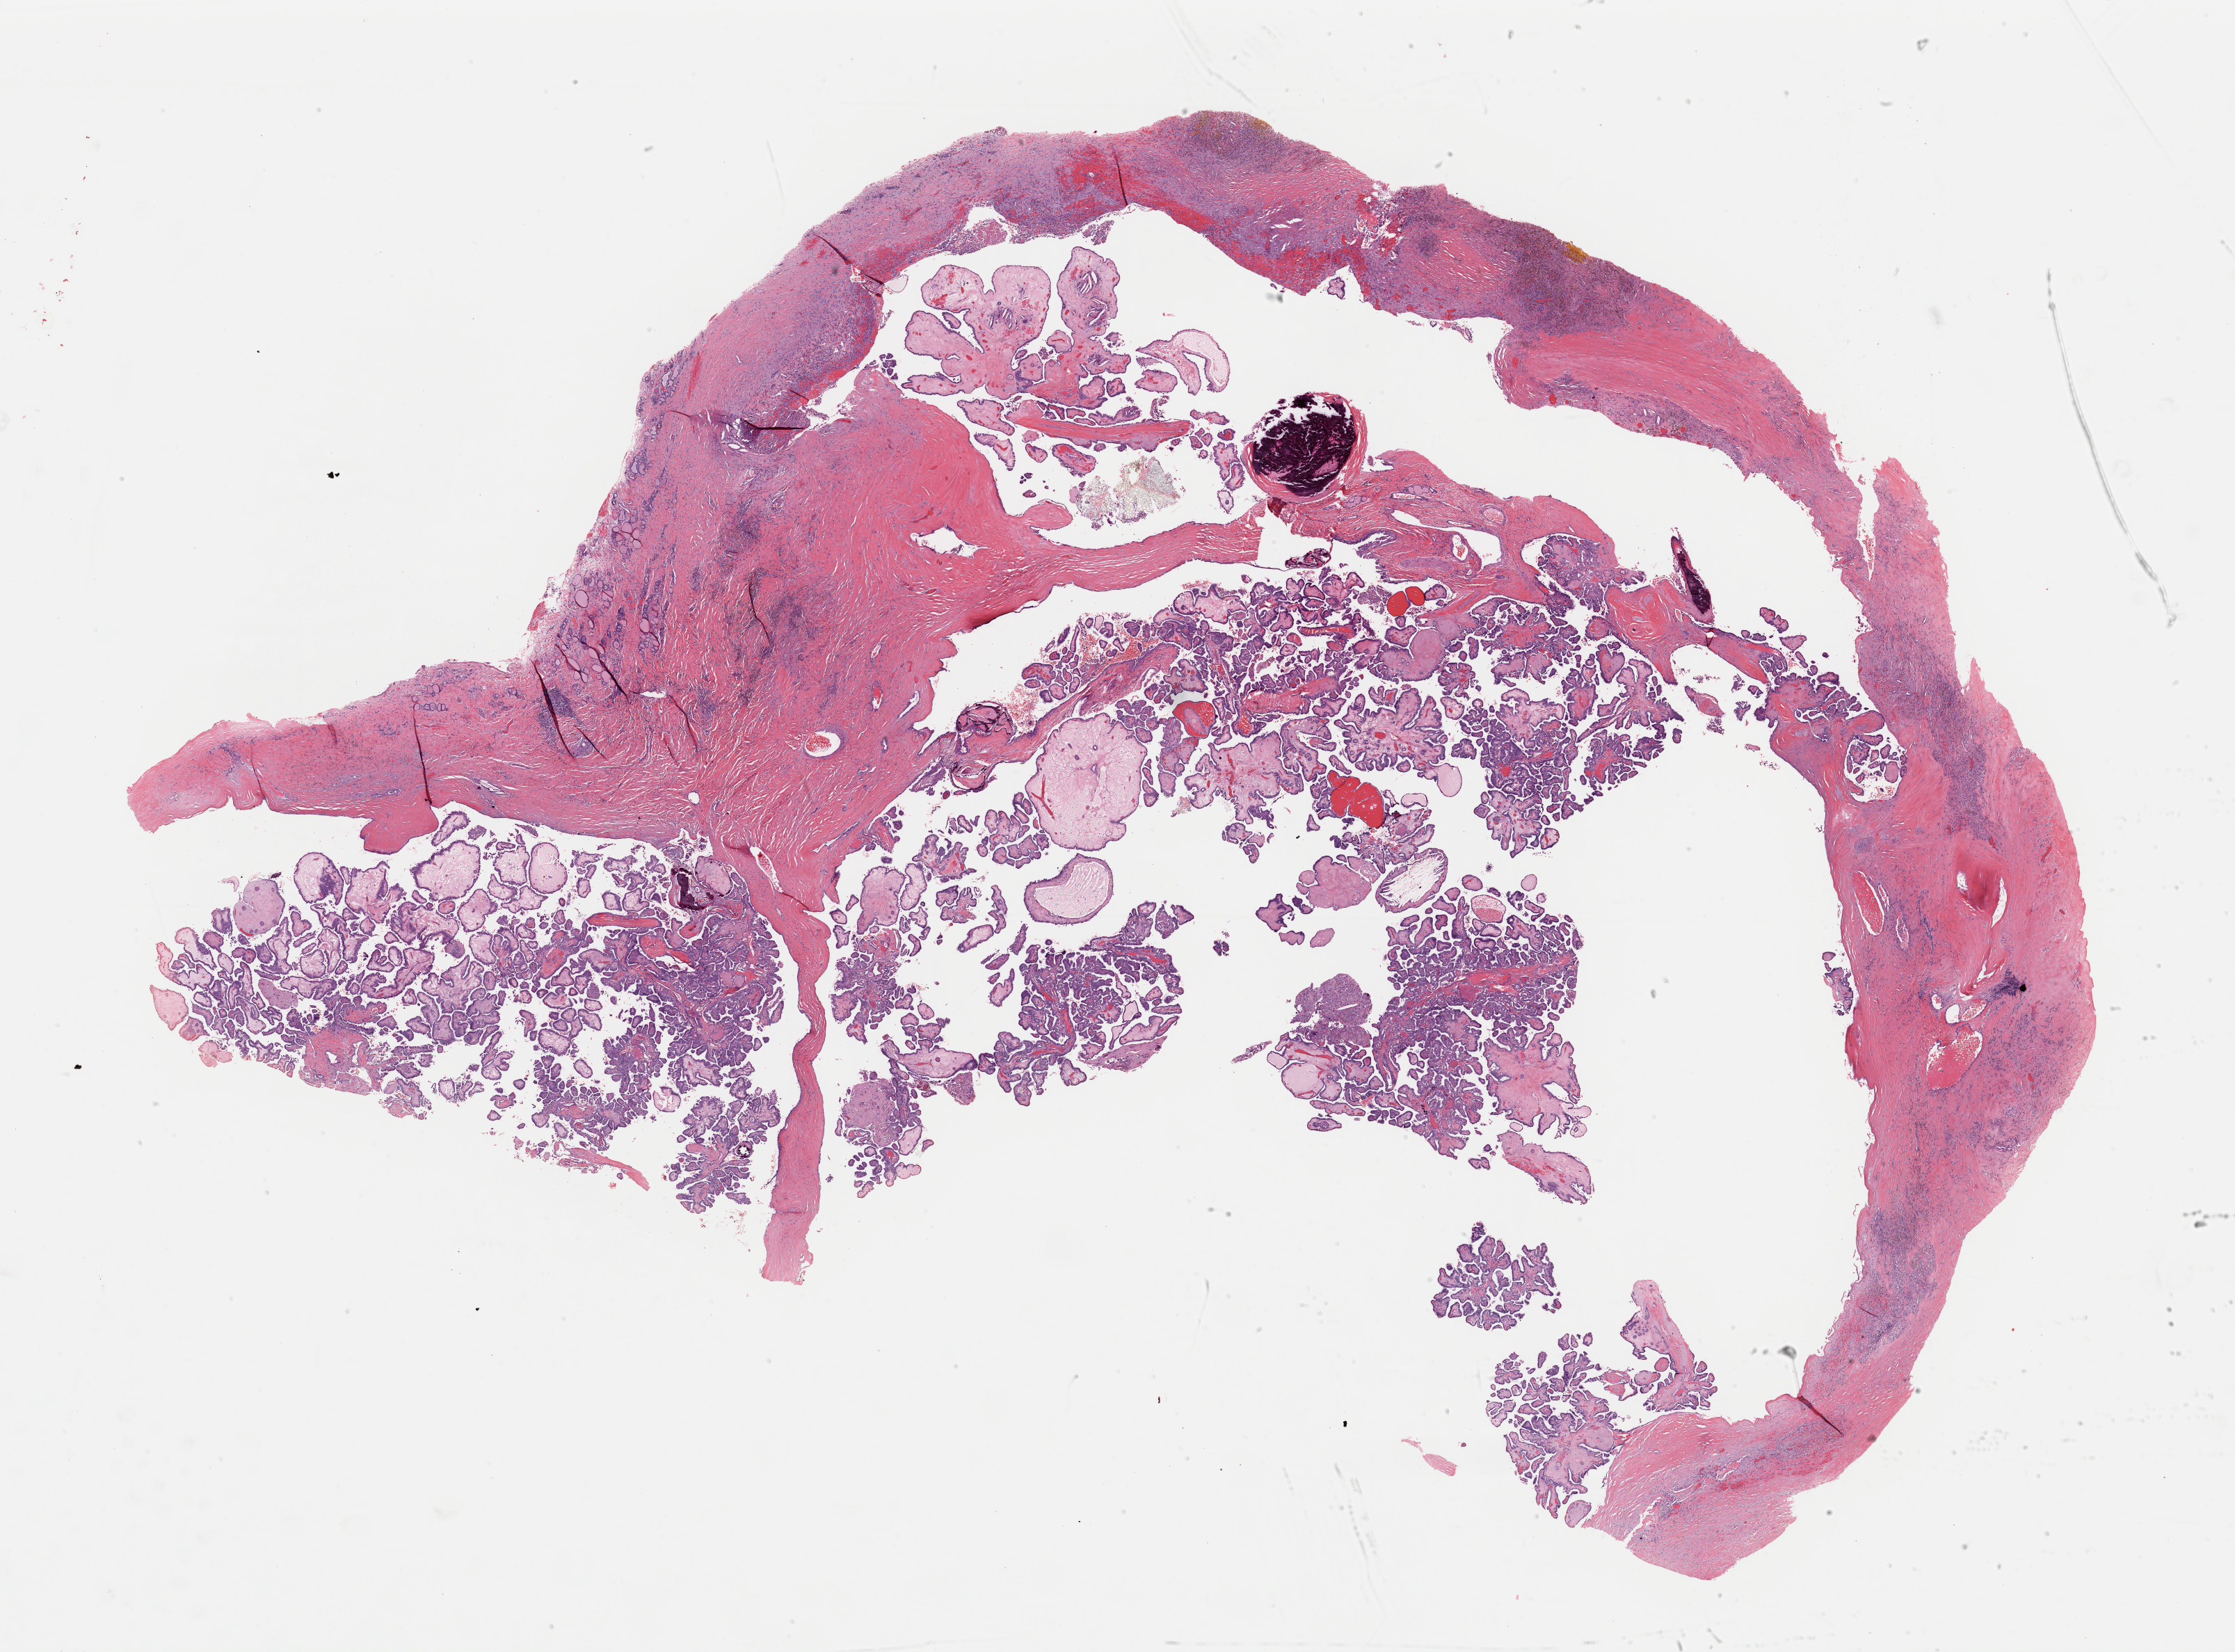
Whole-slide histology image, Hematoxylin and eosin (H&E) stained, a low-resolution overview of the entire scanned area, about 25.4 x 18.8 mm (slide scanned at 40x). Formalin-fixed paraffin-embedded (FFPE) diagnostic section. Thyroid, primary tumour sample. Patient: male, age at initial diagnosis 63 years.
Laterality: left. AJCC pathologic stage: II (5th edition). Histologic diagnosis: Papillary adenocarcinoma, NOS (thyroid gland).